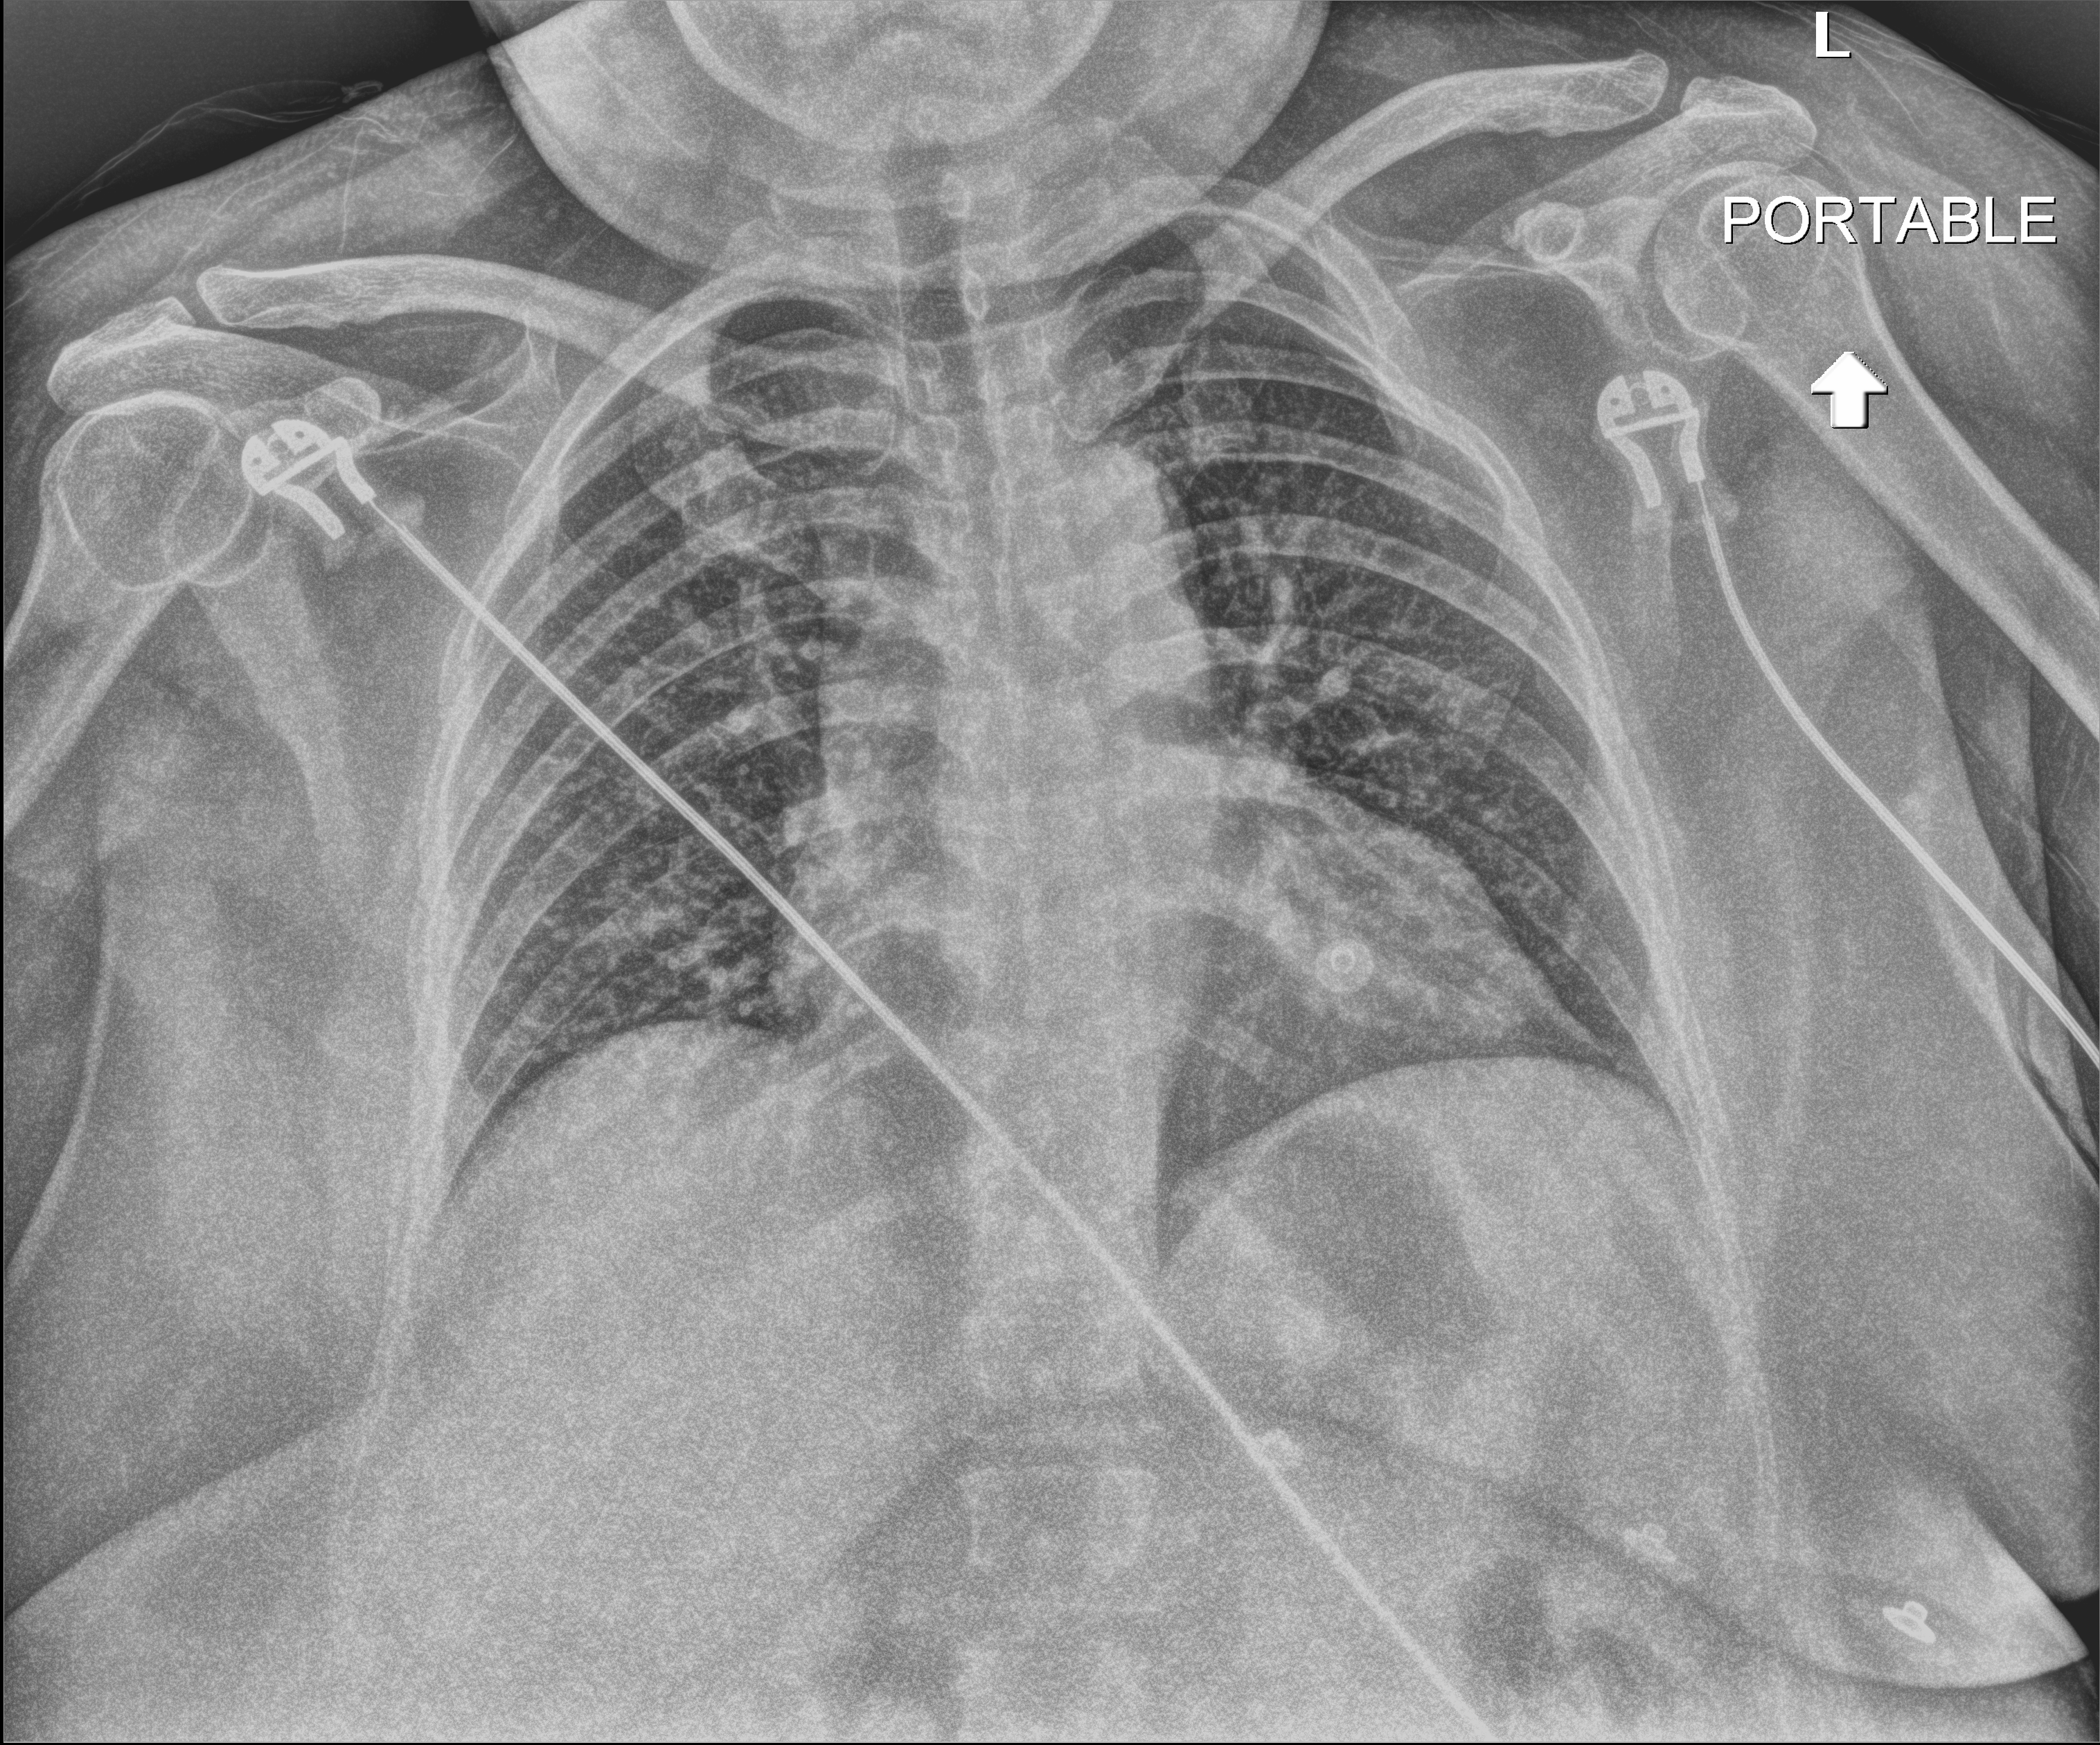
Chest radiograph (digital radiography); anteroposterior (AP) projection. Patient hospitalised with COVID-19; female, aged 18–59 years.
Admission-level facts for this patient (not findings on this image; timing relative to this image not recorded): mechanically ventilated during this hospital stay: no; admitted to intensive care during this hospital stay: no.